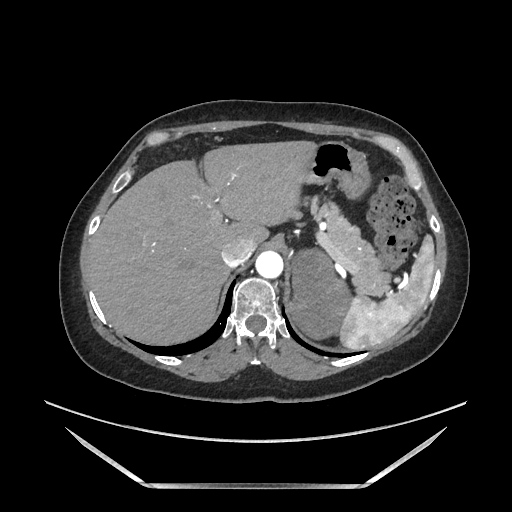
Contrast-enhanced abdominal CT, one axial slice. Slice 139 of 205 in the series (ordered by position). Soft-tissue window (W 400 / L 40 HU). 512 × 512 image matrix, field of view 440 × 440 mm. Female patient. Case-level facts recorded for this patient, not image findings: diagnosis: adrenocortical carcinoma; tumour side: left adrenal; tumour size at pathology: 12.5 cm; Ki-67 index: 39 %; stage (as recorded): 3.
Structures marked on this image (semi-automatically segmented with operator editing):
- mass: bounding box <291,250,350,337> (left, top, right, bottom; pixels)